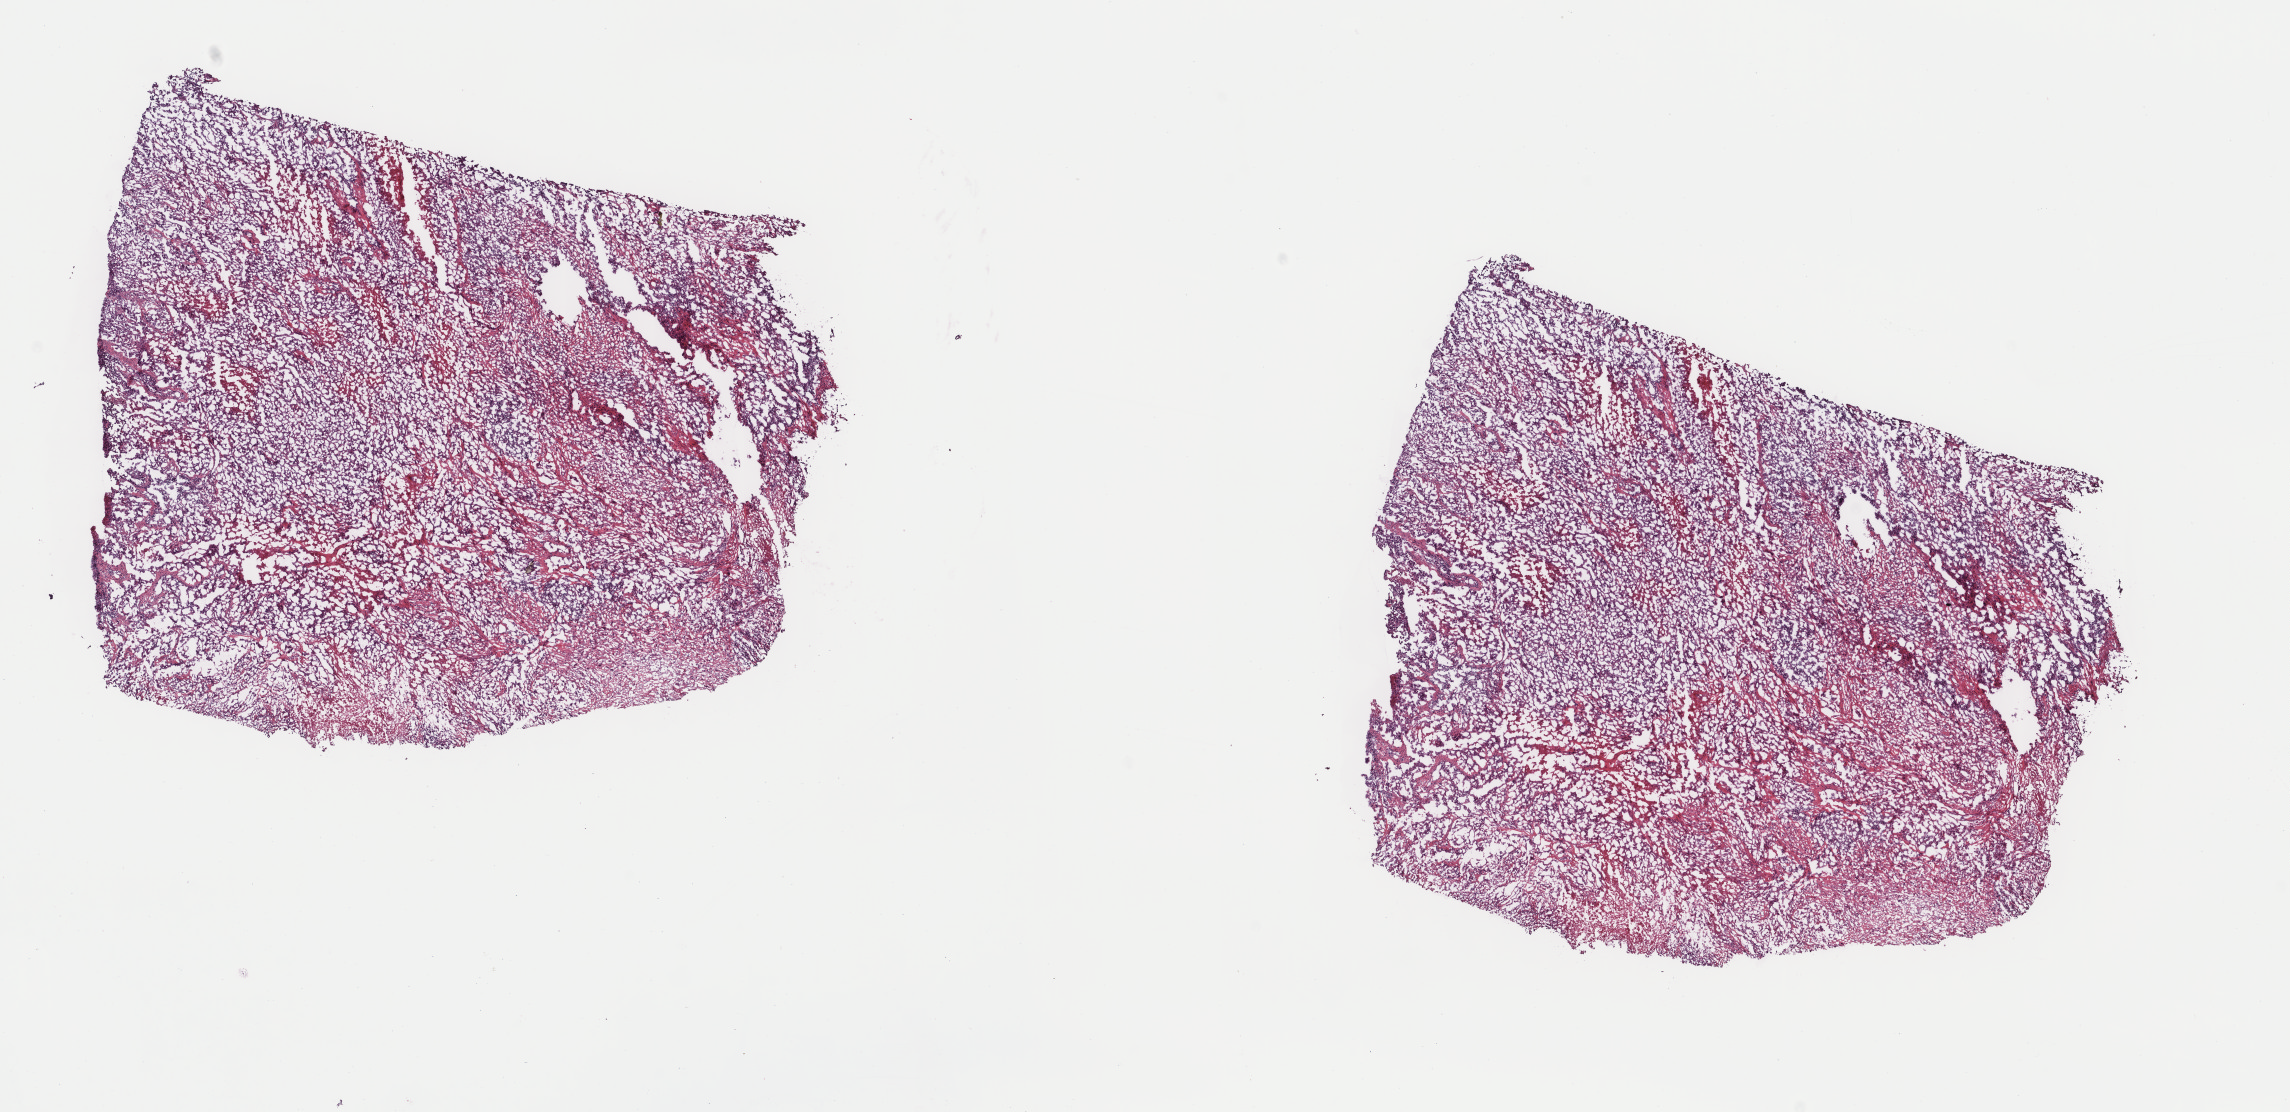
Digitized H&E tissue section (whole slide), whole scanned area (about 18.2 x 8.8 mm, slide scanned at 40x) shown as a low-resolution overview; frozen section from the top of the tissue portion; primary tumour sample from the mesothelium. Male patient; age at initial diagnosis 63 years.
Pathologic diagnosis: Epithelioid mesothelioma, malignant (pleura, NOS).